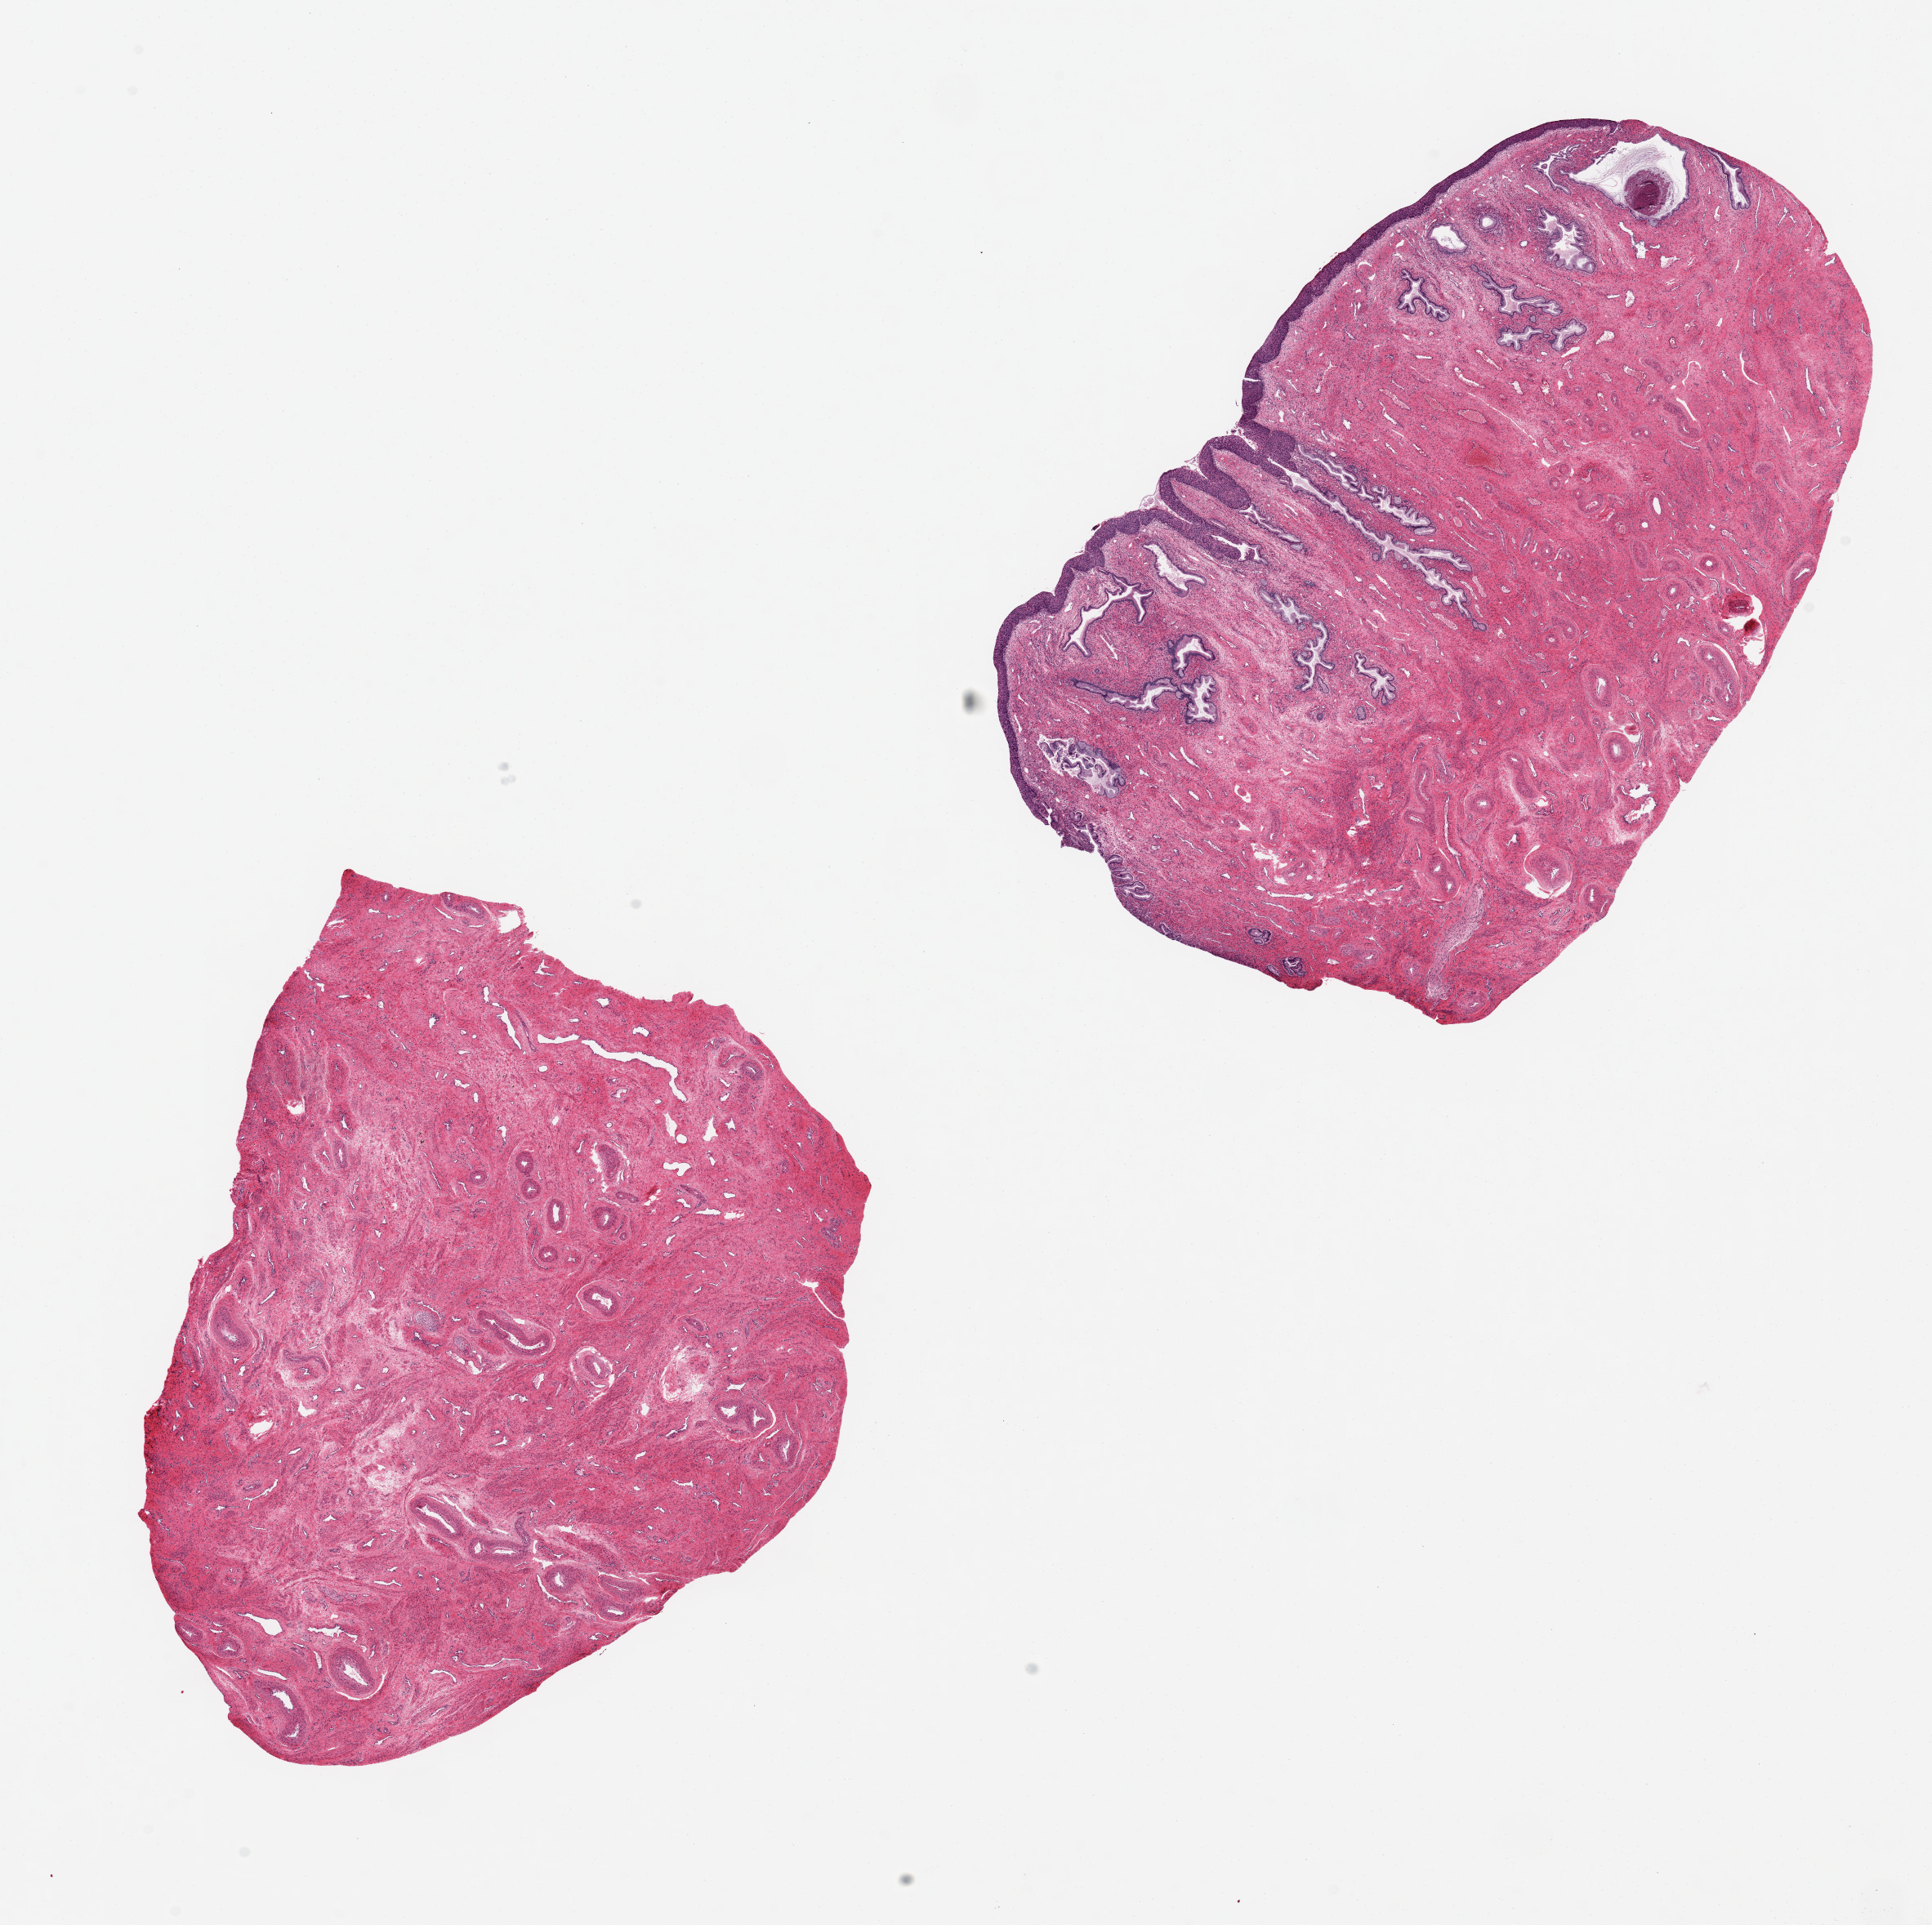
Haematoxylin and eosin whole-slide image, shown as a low-resolution overview of the whole scanned area (about 18.7 x 18.6 mm), PAXgene-fixed paraffin-embedded (PFPE) section, section of endocervix (target tissue), donor tissue sample. Donor sex: female.
• reviewer comment on this tissue sample: 2 pieces, 9x6 & 8x7 mm; 1 piece with squamous high grade dysplasia (11 mm in length); 1 piece without epithelium